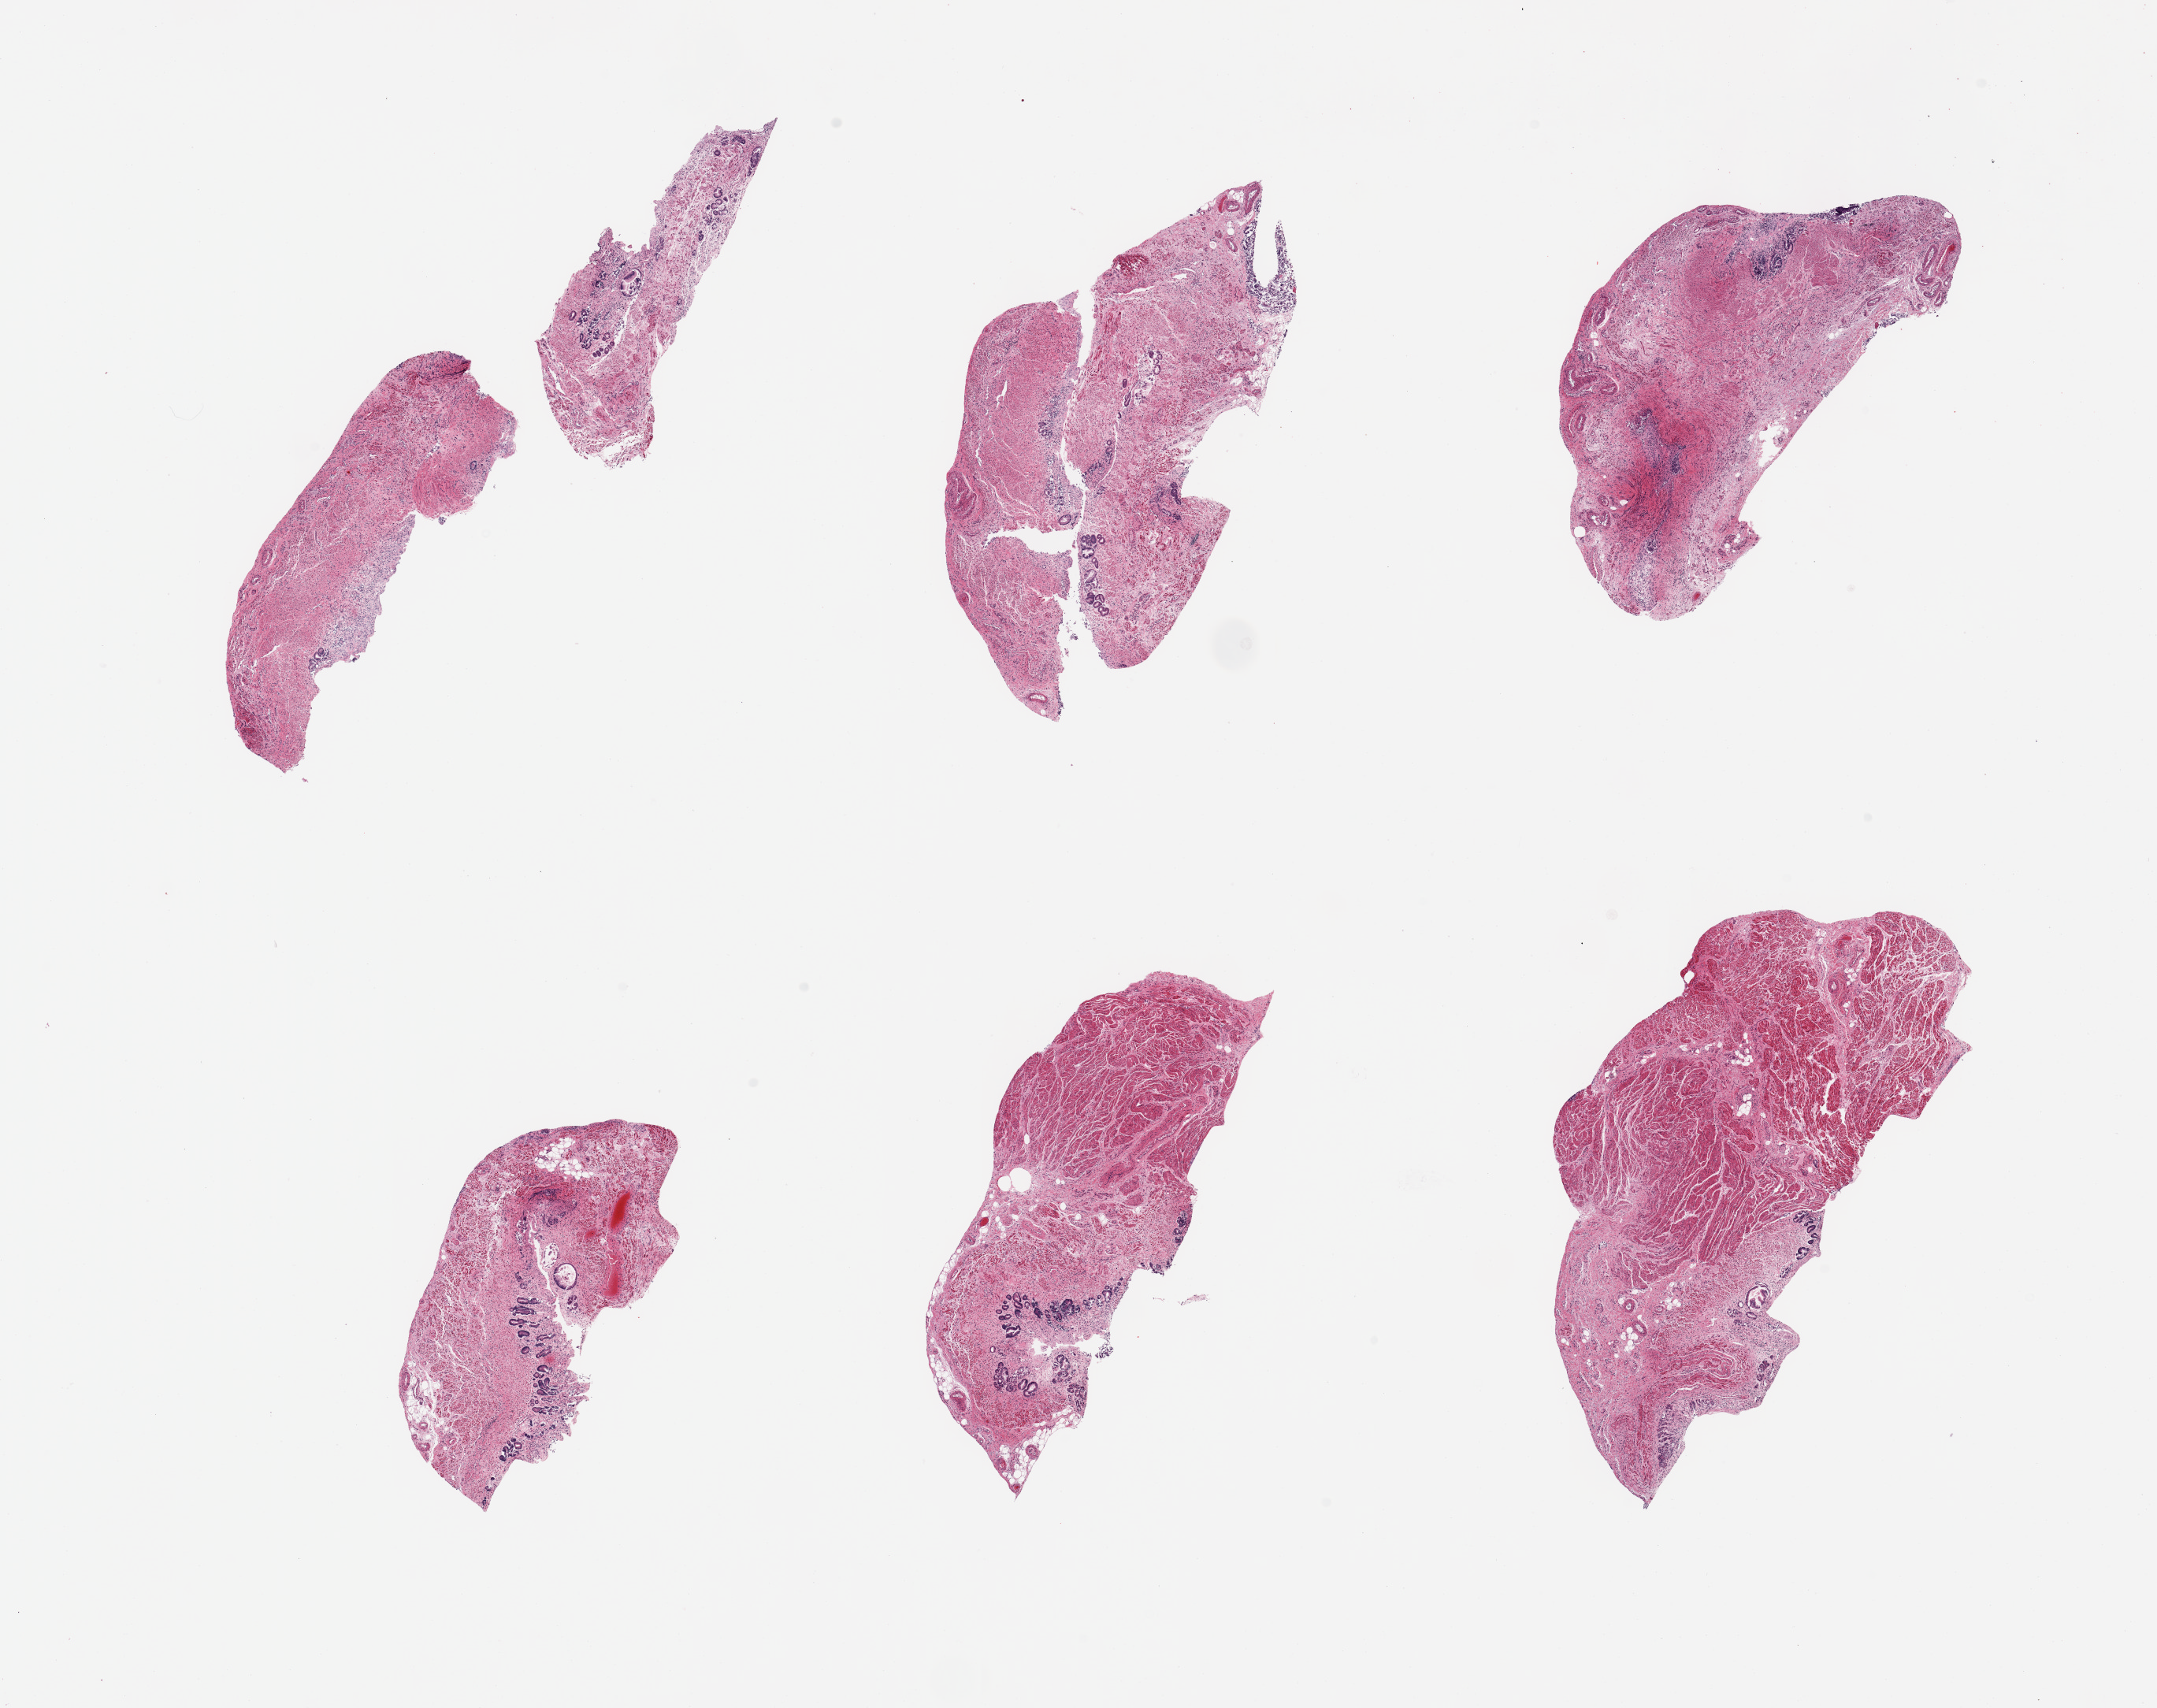
Hematoxylin and eosin (H&E) whole-slide image — a low-resolution overview of the entire scanned area, about 21.7 x 17.1 mm. PAXgene-fixed paraffin-embedded (PFPE) section. Sampled site (target tissue): esophageal mucous membrane. Tissue donor sample. Donor: male.
Pathologist's review note for this sample: 6 pieces; autolyzed glandular mucosa & submucosa; no squamous epithelium.